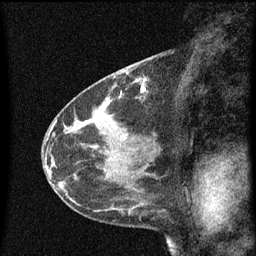
Breast MRI (dynamic contrast-enhanced), one sagittal slice; slice 28 of 60 in the series (ordered by position); dynamic contrast-enhanced series, image 2 of 3 at this slice position (ordered by acquisition); 1.5 T; TE 4.2 ms, TR 8 ms; 2 mm slice thickness; 256 × 256 image matrix. Patient: female, 41 years.
Annotated regions visible in this slice (semi-automatically segmented with operator editing):
- analysis volume of interest (the breast-tissue region the enhancement analysis was run in; not a lesion): bounding box (x1, y1, x2, y2) in pixels: (130, 76, 155, 103)
- tumour enhancement mask (voxels above the 70 % enhancement threshold inside the analysis volume of interest): (140, 78, 147, 99)